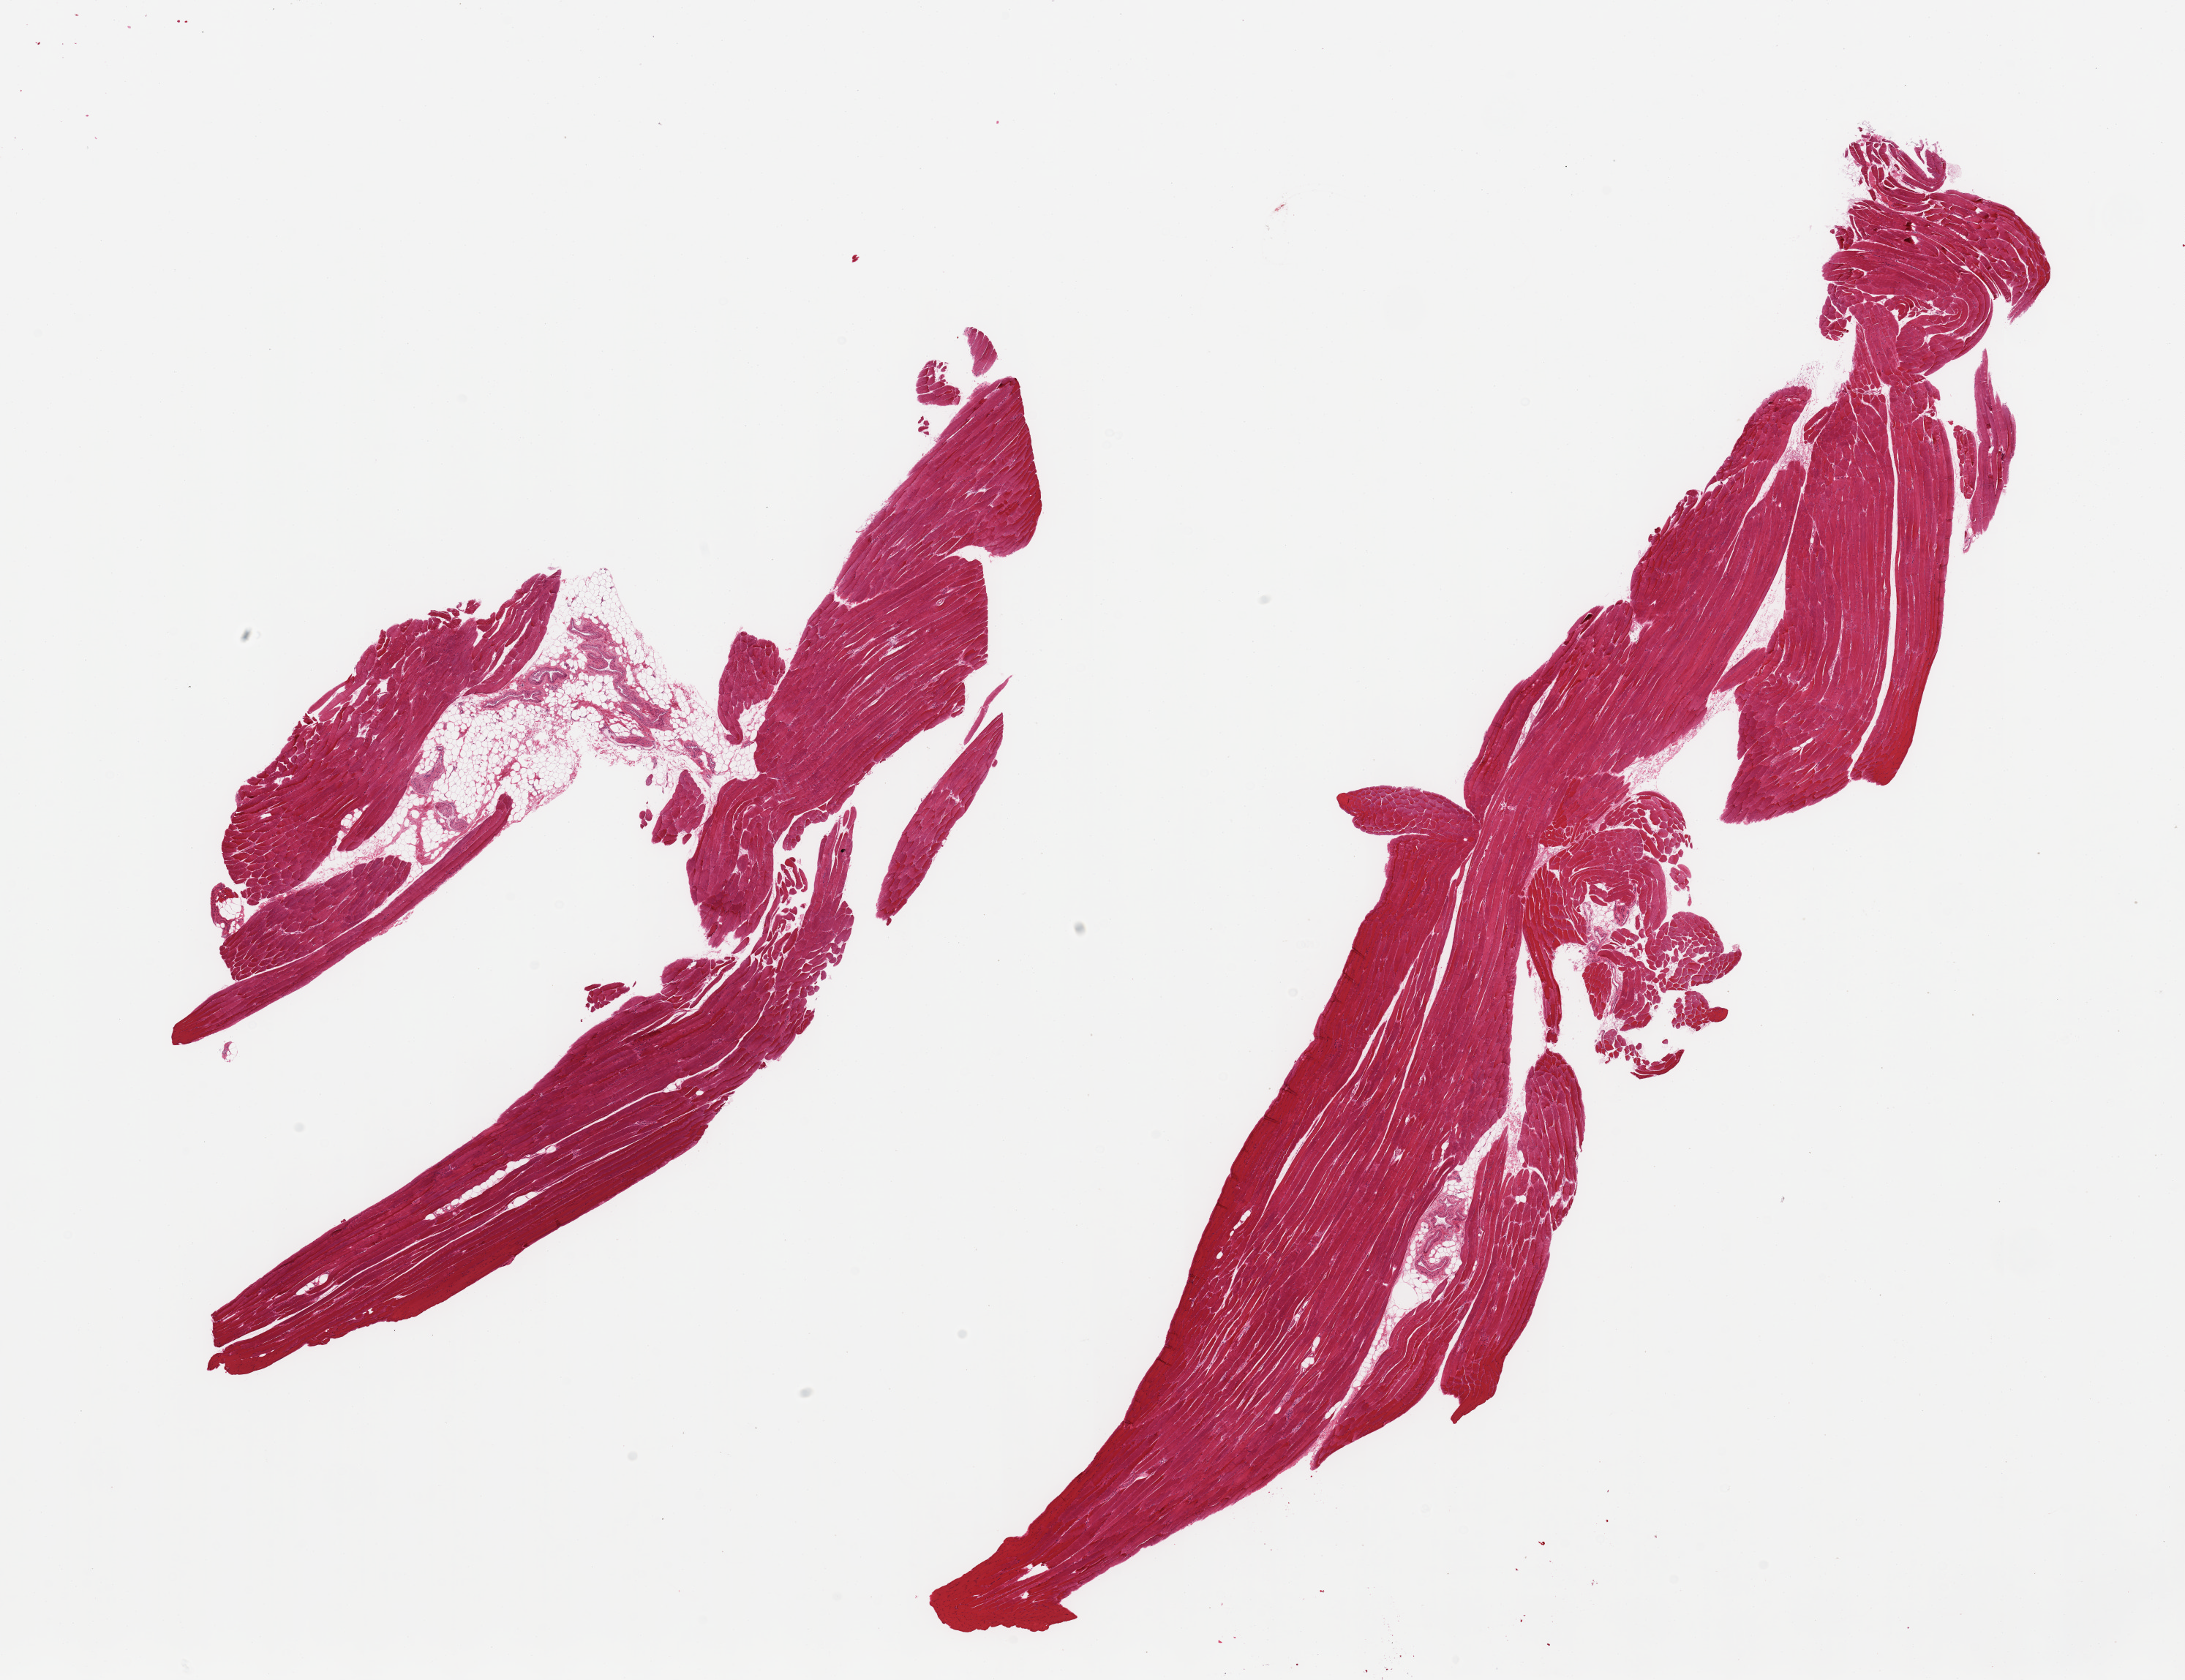
Hematoxylin and eosin (H&E) whole-slide image, brightfield, whole scanned area (about 23.6 x 18.2 mm) shown as a low-resolution overview; PAXgene-fixed paraffin-embedded (PFPE) section; section of skeletal muscle (target tissue); tissue donor sample.
Pathologist's review note for this sample: 2 pieces, ~10% interstitial fat/vascular elements.